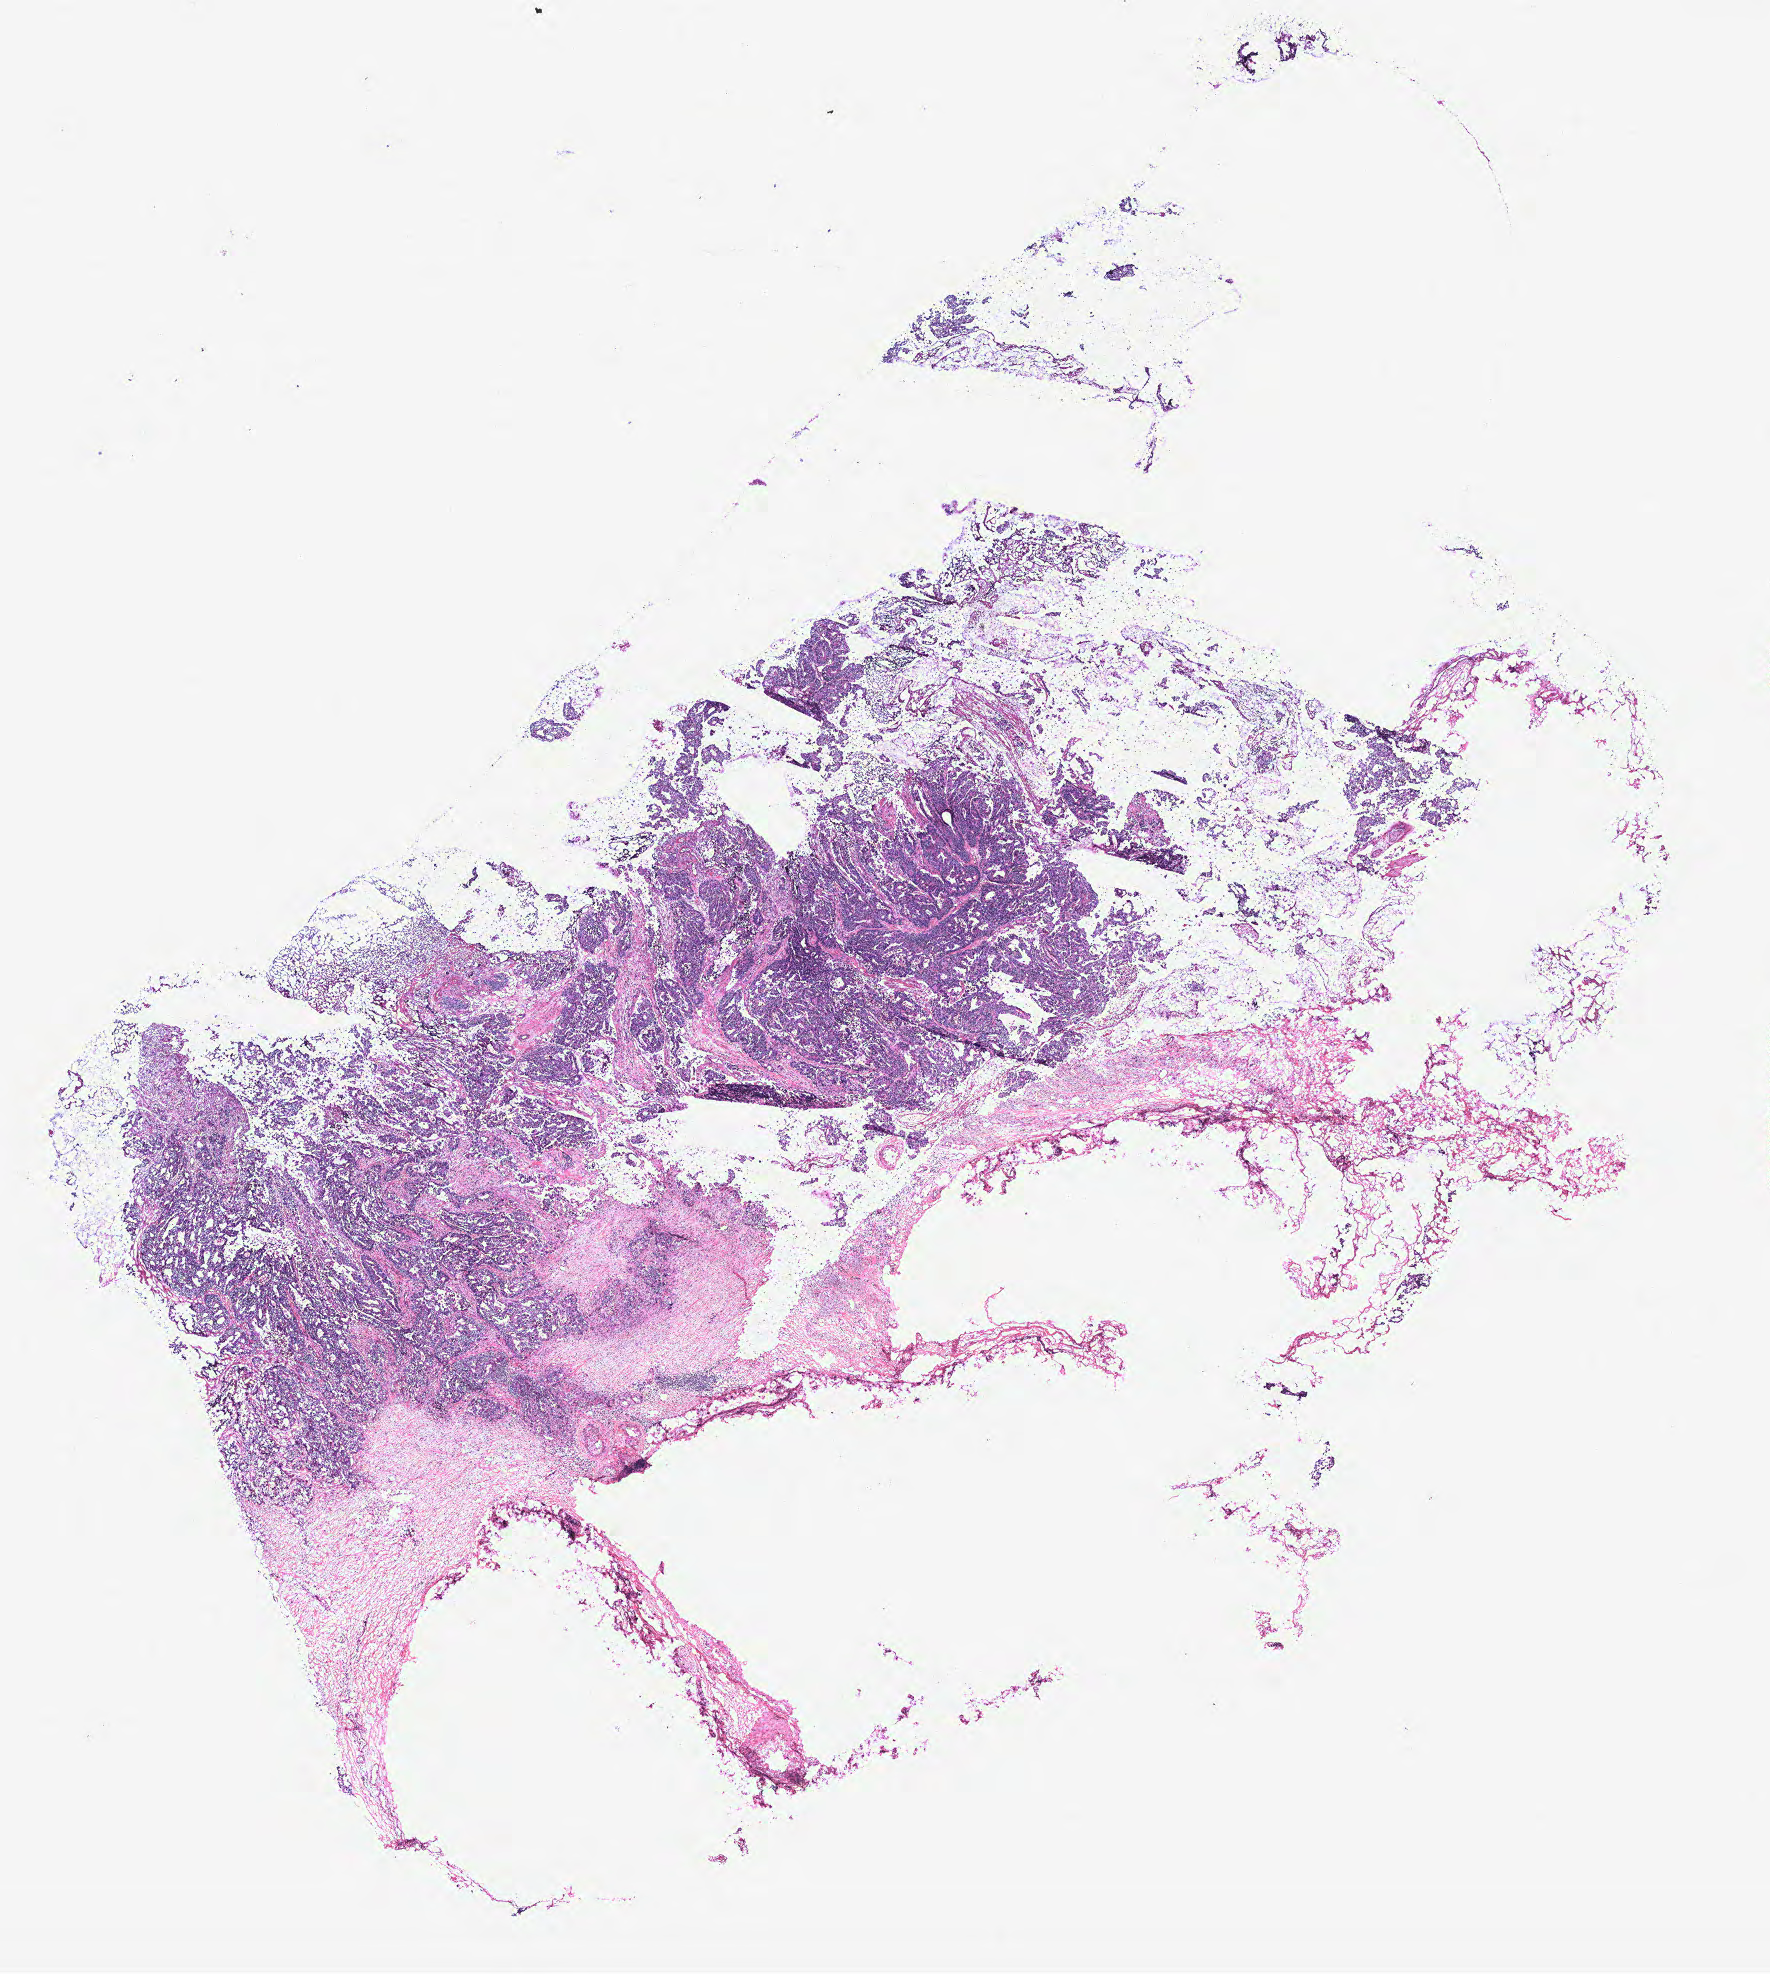
Digitized H&E-stained tissue section (whole slide), whole scanned area (about 14.2 x 15.8 mm, acquisition: 40x scan) shown as a low-resolution overview. Normal (non-tumour) tissue sample, colon. Female, 75 y/o.
This section: normal (non-tumour) tissue from the same patient. Patient diagnosis: Adenocarcinoma, NOS.